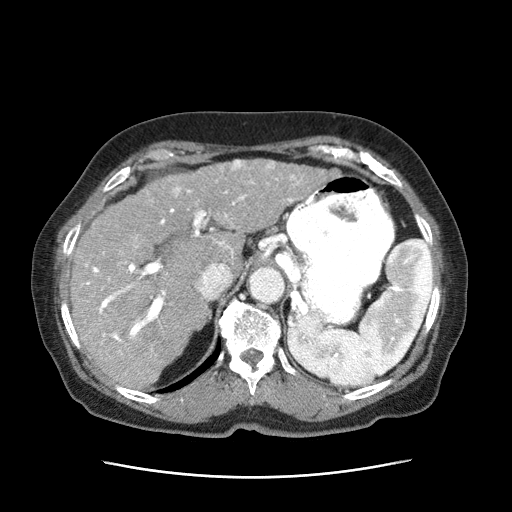
Contrast-enhanced abdominal CT (liver protocol), one axial slice. Position 45 of 63 along the scan axis. Reconstruction kernel STANDARD. 120 kVp. Intravenous contrast given. Soft-tissue window (W 400 / L 40 HU). 2.5 mm slice thickness. 512 × 512 image matrix. Female patient, age 79 years. Case-level facts recorded for this patient, not image findings: diagnosis: hepatocellular carcinoma (patient treated with transarterial chemoembolisation; whether this scan precedes or follows treatment is not stated here); TNM stage (as recorded): Stage-II; Child-Pugh class: B; tumour differentiation: well differentiated; tumour nodularity: multinodular.
Structures marked on this image (semi-automatic segmentation, software-assisted and operator-edited):
- abdominal aorta: box from (x=248, y=269) to (x=285, y=304) px
- liver parenchyma outside the tumour (the mass and vessels are separate outlines, so this box may not span the whole liver): (x=70, y=174)–(x=250, y=392)
- mass: (x=177, y=160)–(x=331, y=234)
- liver vessels: (x=86, y=178)–(x=299, y=342)